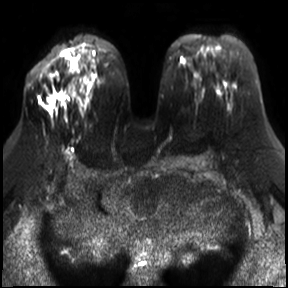
Breast MRI, one axial slice; slice 16 of 30 in the series (ordered by position); diffusion-weighted series; image 2 of 4 stored at this slice position (different b-values; order by instance number); 3 T; 288 × 288 image matrix, field of view 340 × 340 mm. Female patient.
Annotated regions visible in this slice (expert manual segmentation):
- tumour on diffusion-weighted imaging: bounding box (x1, y1, x2, y2) in pixels: (48, 95, 60, 110)